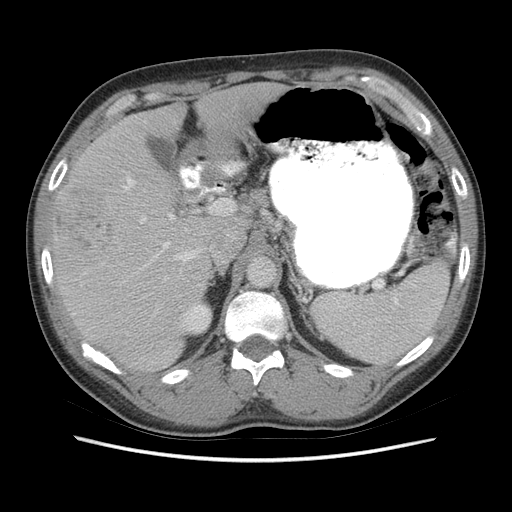
Contrast-enhanced abdominal CT (liver protocol), one axial slice. Position 41 of 73 along the scan axis. Reconstruction kernel STANDARD. 140 kVp. Soft-tissue window (W 400 / L 40 HU). 2.5 mm slice thickness. 512 × 512 image matrix, field of view 360 × 360 mm. Case-level facts recorded for this patient, not image findings: diagnosis: hepatocellular carcinoma (patient treated with transarterial chemoembolisation; whether this scan precedes or follows treatment is not stated here); TNM stage (as recorded): Stage-IIIA; Child-Pugh class: A; tumour nodularity: multinodular.
Annotated regions visible in this slice (semi-automatically segmented with operator editing):
- liver parenchyma outside the tumour (the mass and vessels are separate outlines, so this box may not span the whole liver): box from (x=50, y=82) to (x=286, y=372) px
- mass: (x=53, y=188)–(x=113, y=257)
- liver vessels: (x=124, y=178)–(x=234, y=267)